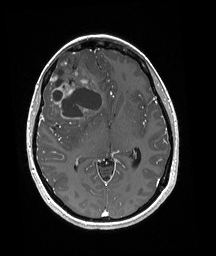
Brain MRI from a brain-tumour surgery series, one axial slice. Position 103 of 192 along the scan axis. T1-weighted post-contrast. 216 × 256 image matrix, field of view 211 × 250 mm. From the clinical record (not read from this slice): histopathology: Oligodendroglioma; WHO grade: 3; IDH mutation: yes; tumour location: Right Frontal.
Structures marked on this image (expert manual segmentation):
- tumour: bounding box (x1, y1, x2, y2) in pixels: (48, 52, 102, 119)